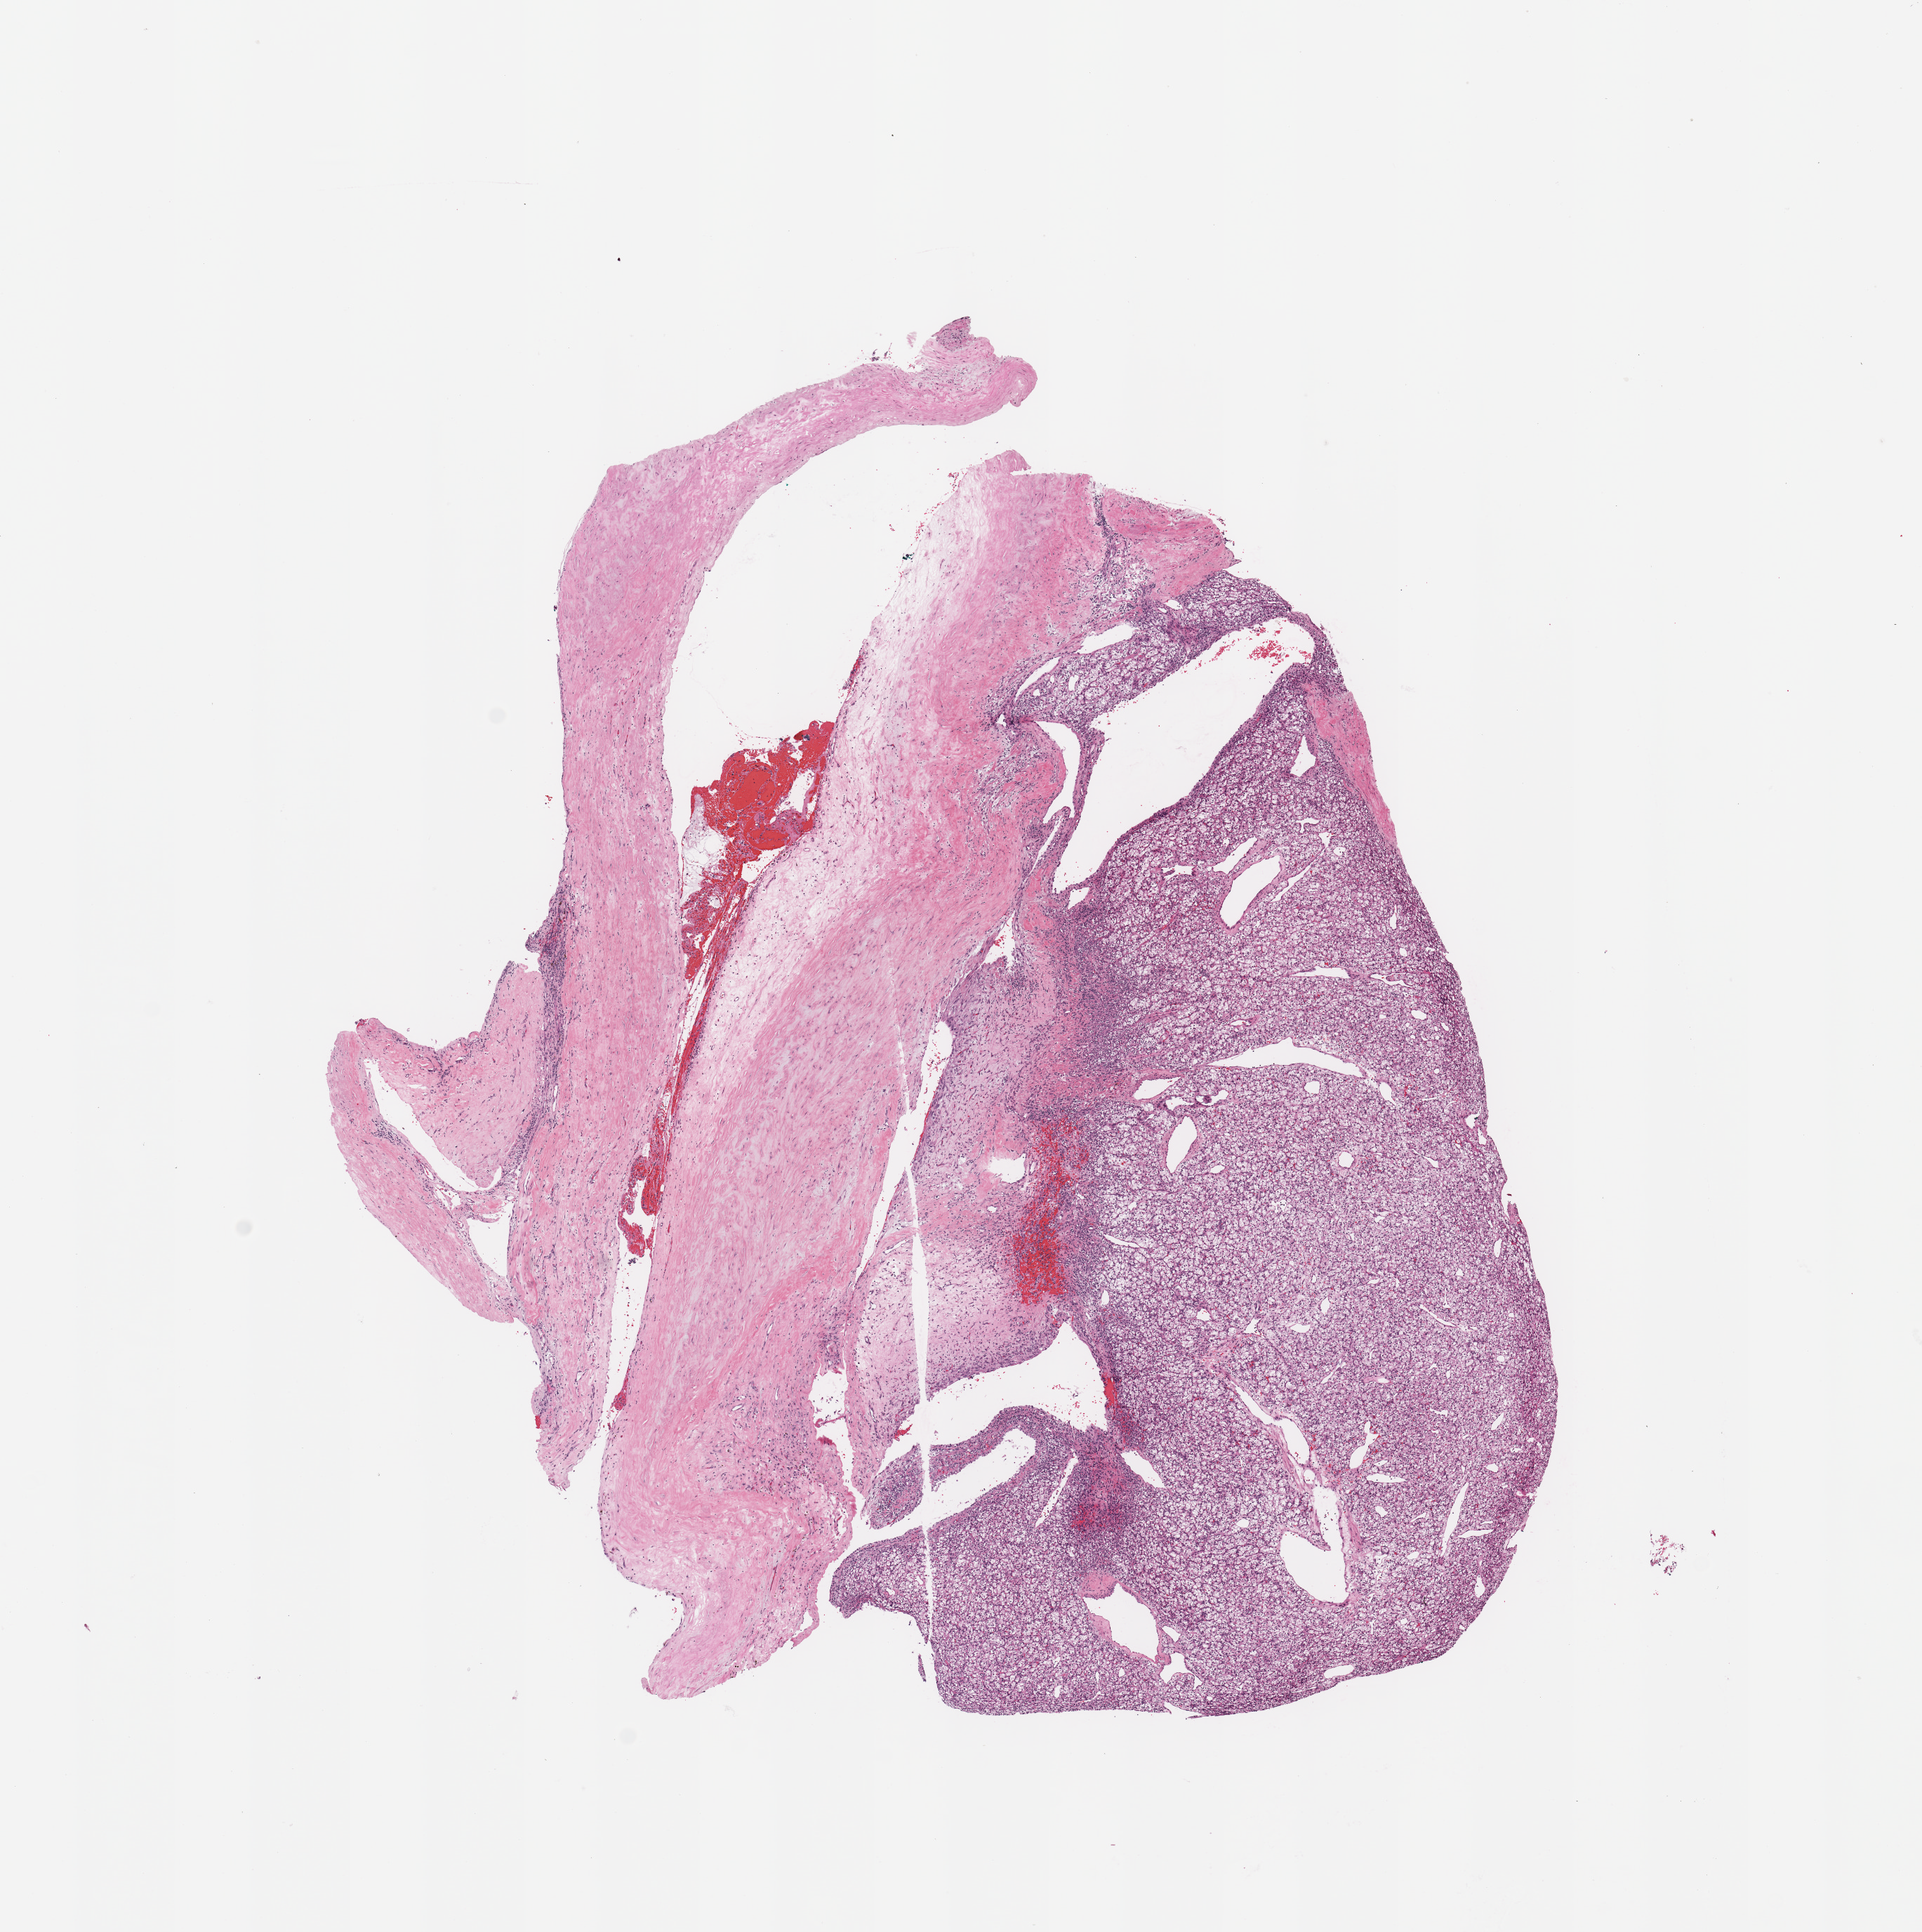
Digitized Hematoxylin and eosin (H&E) stained tissue section (whole slide), whole scanned area (about 10.8 x 10.9 mm) shown as a low-resolution overview, kidney, tumour tissue. Female, 59 y/o. Histologic grade: G2 (moderately differentiated).
Diagnosis: Renal cell carcinoma, NOS. Primary tumour site (as recorded): lower pole. AJCC pathologic stage: I.